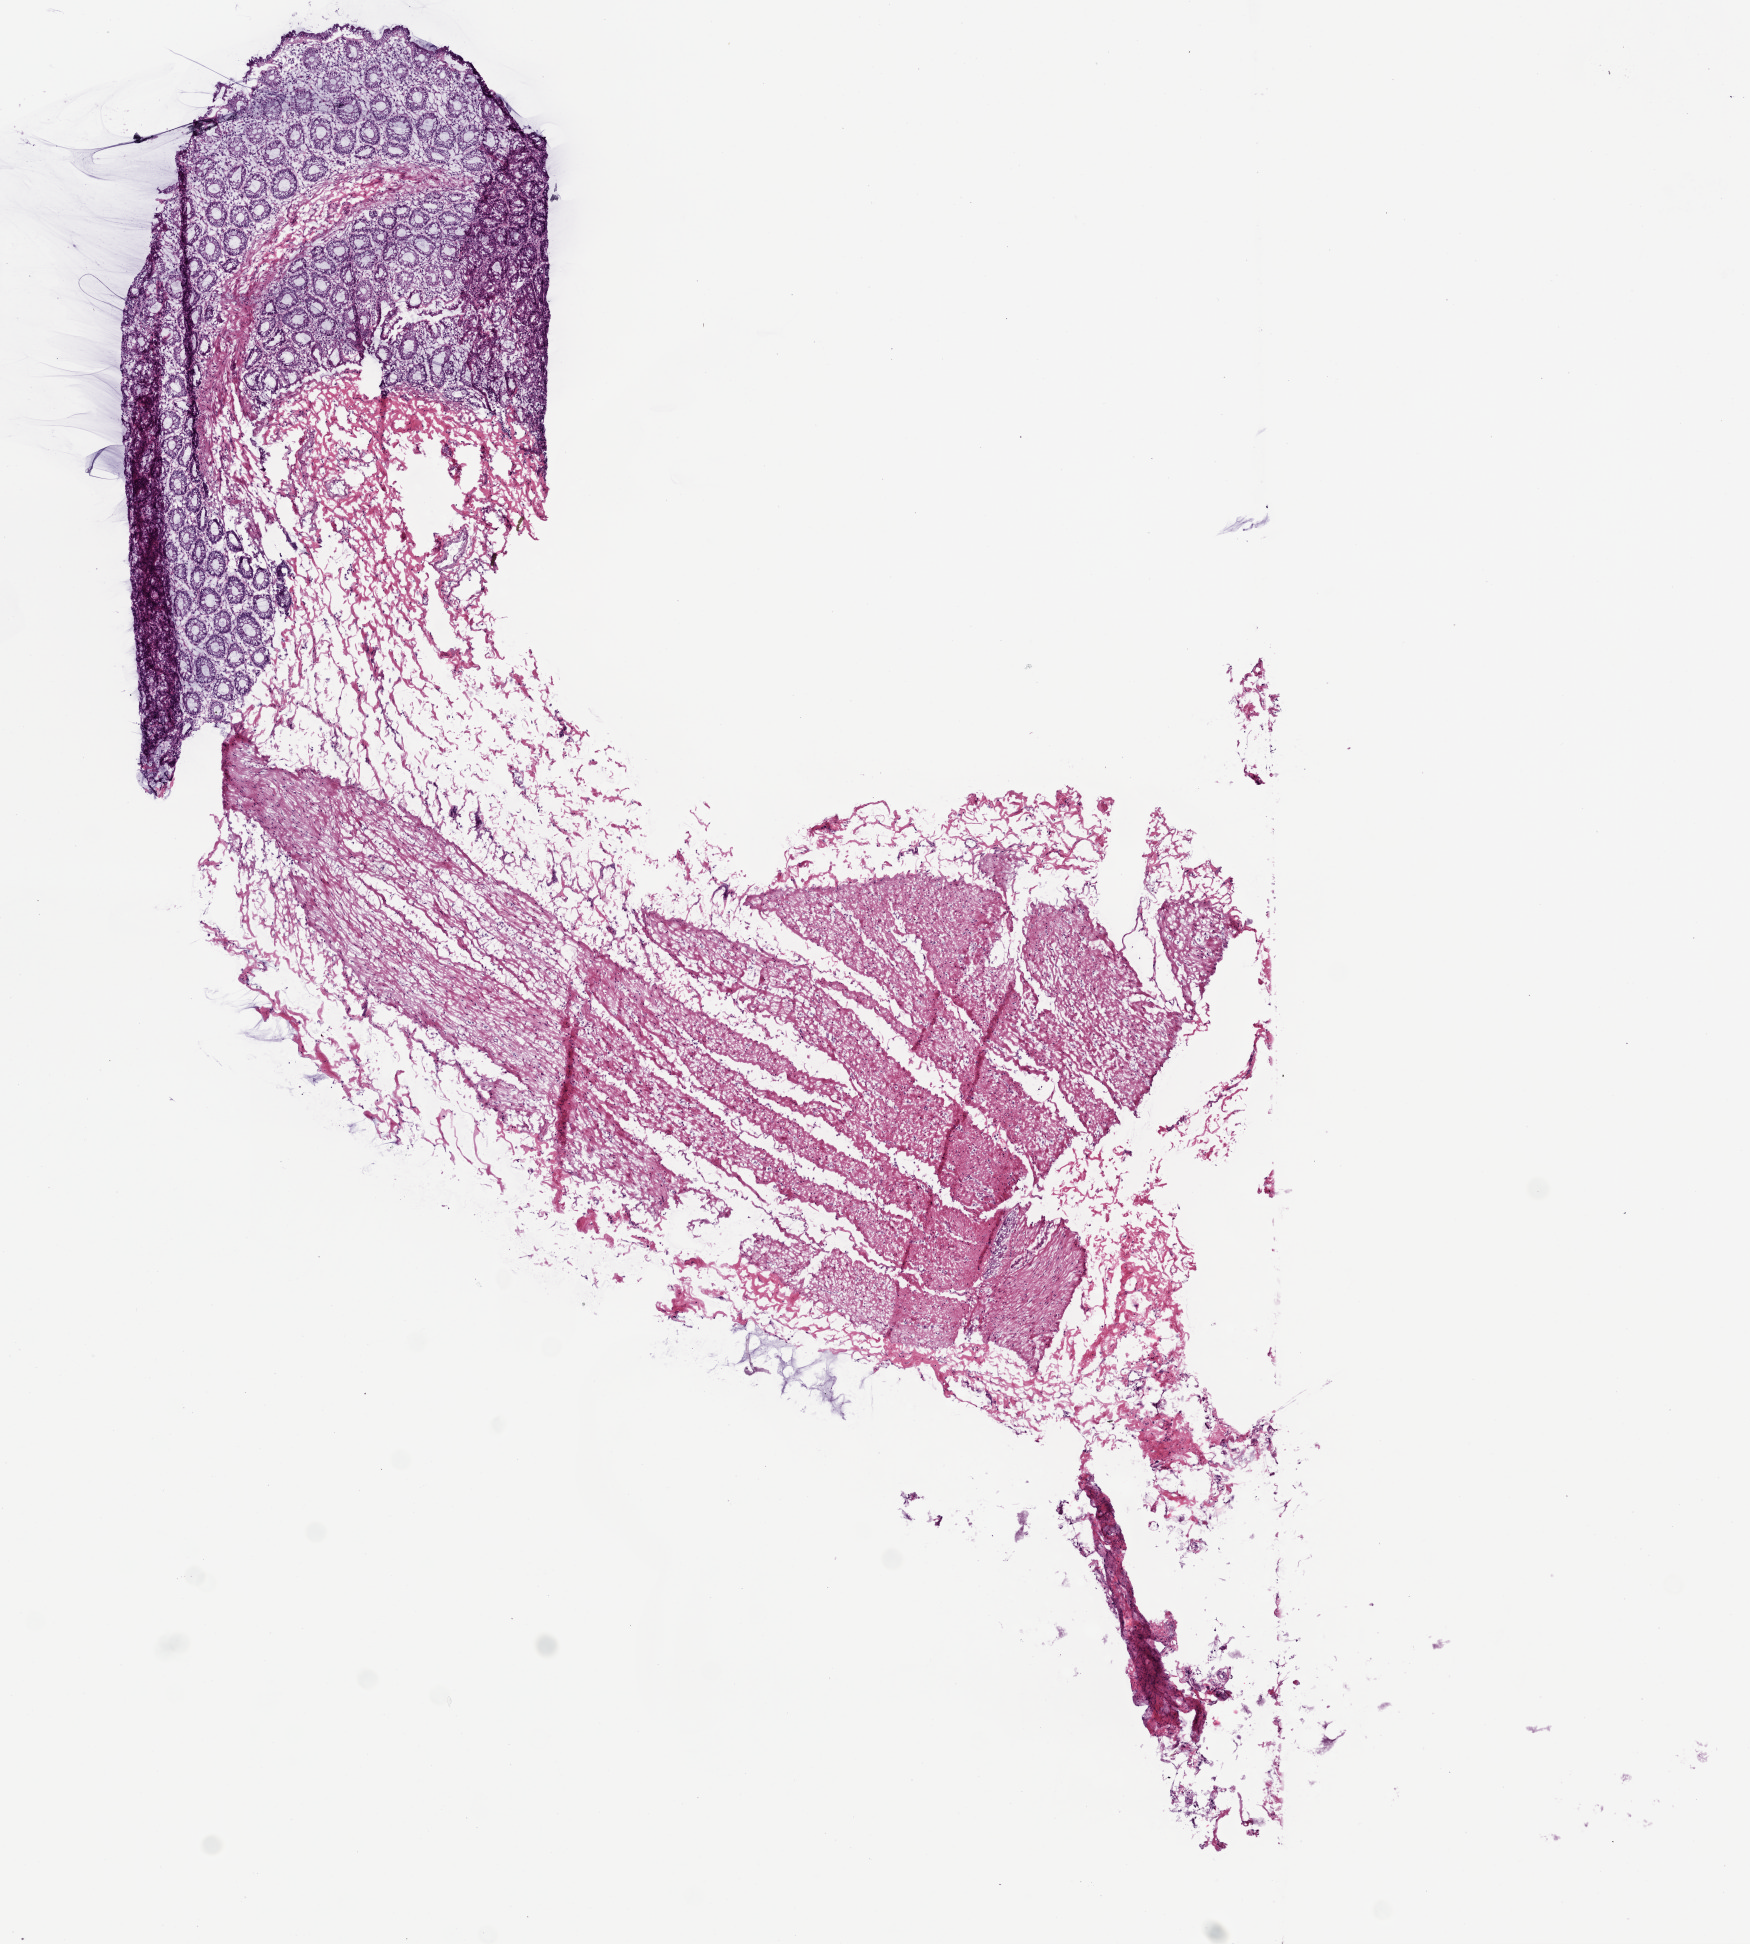
Whole-slide histology image, H&E-stained — shown as a low-resolution overview of the whole scanned area (about 7.0 x 7.8 mm, acquisition: 20x scan). Frozen section from the top of the tissue portion. Solid tissue normal (non-tumour tissue) sample from the rectum. Patient: male, age at initial diagnosis 65 years.
This section: solid tissue normal (non-tumour) sample from the same patient. Patient diagnosis: Adenocarcinoma, NOS.